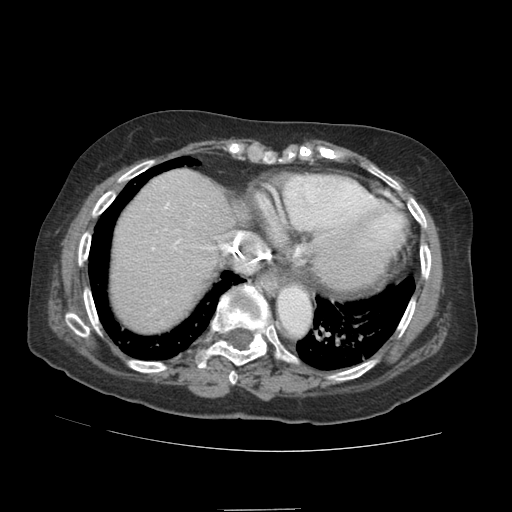
Contrast-enhanced abdominal CT (liver protocol), one axial slice. Slice 77 of 89 in the series (ordered by position). Reconstruction kernel STANDARD. 140 kVp. Soft-tissue window (W 400 / L 40 HU). 2.5 mm slice thickness. 512 × 512 image matrix, field of view 360 × 360 mm. Case-level facts recorded for this patient, not image findings: diagnosis: hepatocellular carcinoma (patient treated with transarterial chemoembolisation; whether this scan precedes or follows treatment is not stated here); TNM stage (as recorded): Stage-II; Child-Pugh class: A; tumour differentiation: moderately differentiated; tumour nodularity: multinodular.
Annotated regions visible in this slice (semi-automatic segmentation, software-assisted and operator-edited):
- abdominal aorta: bounding box (x1, y1, x2, y2) in pixels: (278, 287, 310, 334)
- liver parenchyma outside the tumour (the mass and vessels are separate outlines, so this box may not span the whole liver): (112, 170, 248, 332)
- liver vessels: (152, 187, 223, 250)